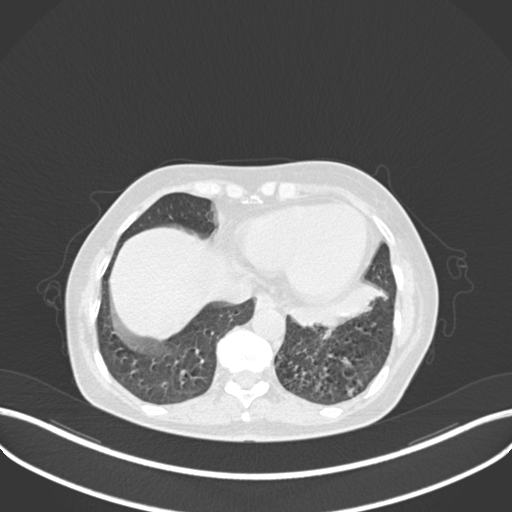
Chest CT, one axial slice; slice 66 of 270 in the series (ordered by position); lung window (W 1500 / L -600 HU); 1 mm slice thickness; 512 × 512 image matrix. Patient: female, 63 years. Case-level facts recorded for this patient, not image findings: clinical TNM (as recorded): T1b N0 M0.
Annotated regions visible in this slice (bounding box drawn by a radiologist):
- lung tumour (recorded histology: adenocarcinoma): bounding box <280,280,391,330> (left, top, right, bottom; pixels)